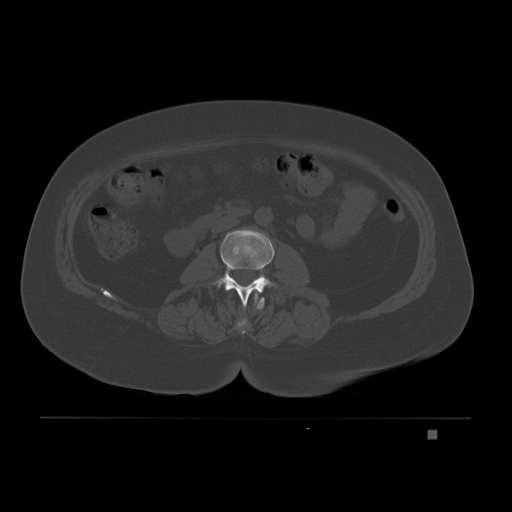
CT including the spine, one axial slice. Position 60 of 221 along the scan axis. Bone window (W 1800 / L 400 HU). 3 mm slice thickness. 512 × 512 image matrix, field of view 474 × 474 mm. Female patient, age 63 years. From the clinical record (not read from this slice): primary cancer: breast.
Structures marked on this image (semi-automatically segmented with operator editing):
- L1 vertebra: bounding box <237,291,262,334> (left, top, right, bottom; pixels)
- L2 vertebra: <197,229,274,308>